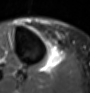
MRI of an extremity soft-tissue mass, one axial slice; position 35 of 60 along the scan axis; STIR; MR volume resampled by the dataset authors to the PET/CT grid (not the native acquisition matrix); 3.27 mm slice thickness; 90 × 93 image matrix, field of view 88 × 91 mm. Female patient. From the clinical record (not read from this slice): histological type: undifferentiated – high grade; grade: high; site of the primary tumour: right thigh.
Structures marked on this image (expert contour drawn on MRI and transferred to this co-registered scan by the dataset authors):
- gross tumour volume (mass): box from (x=44, y=46) to (x=63, y=72) px